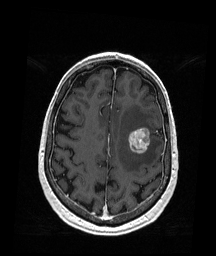
Brain MRI from a brain-tumour surgery series, one axial slice. Slice 58 of 176 in the series (ordered by position). T1-weighted post-contrast. 216 × 256 image matrix, field of view 211 × 250 mm. Case-level facts recorded for this patient, not image findings: histopathology: Metastatic Melanoma.
Annotated regions visible in this slice (expert manual segmentation):
- tumour: bounding box <128,128,151,154> (left, top, right, bottom; pixels)